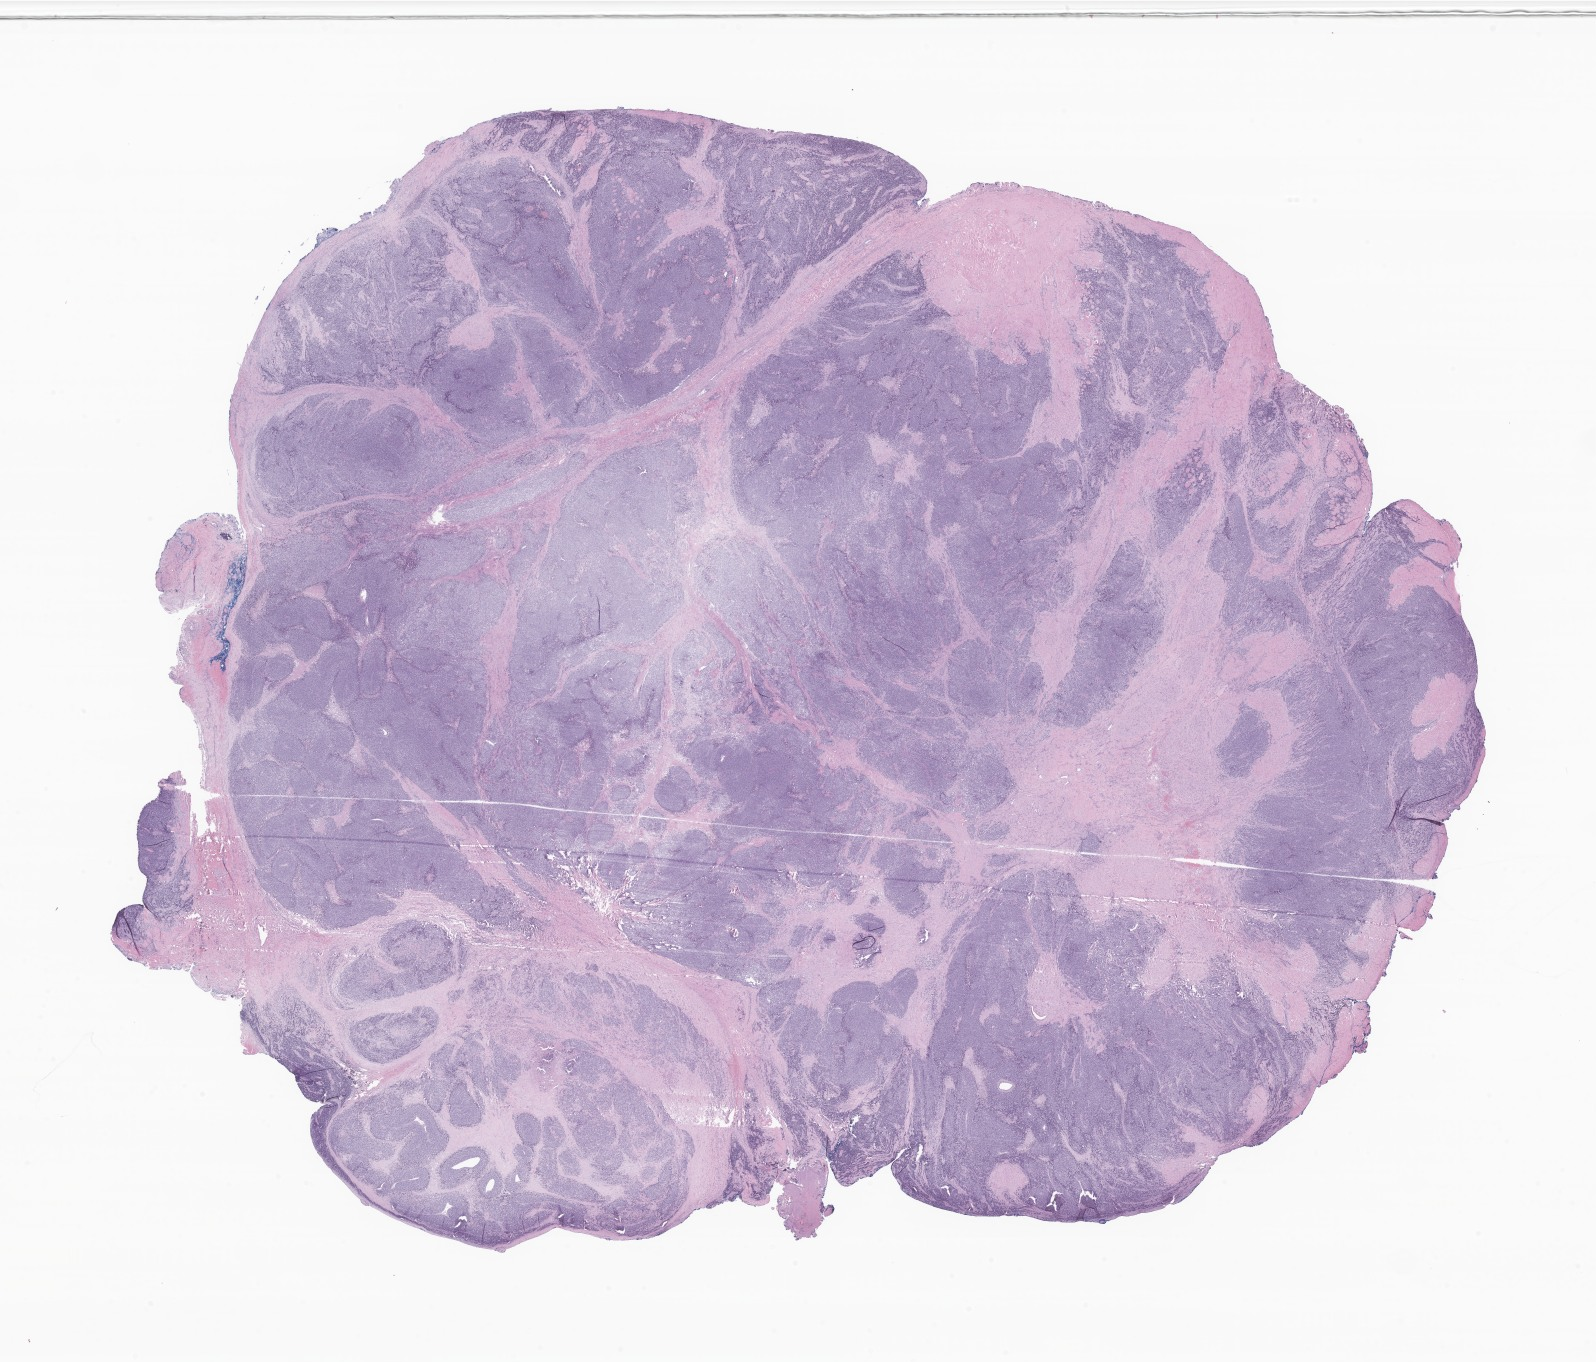
Digitized H&E-stained section of tumor tissue from the lower limb — shown as a low-resolution overview of the whole scanned area (about 26.9 x 23.0 mm). Formalin-fixed, paraffin-embedded (FFPE) tissue. Male patient, age 218 months (18 years 2 months).
Diagnosis (ICD-O-3 morphology term): Alveolar rhabdomyosarcoma.